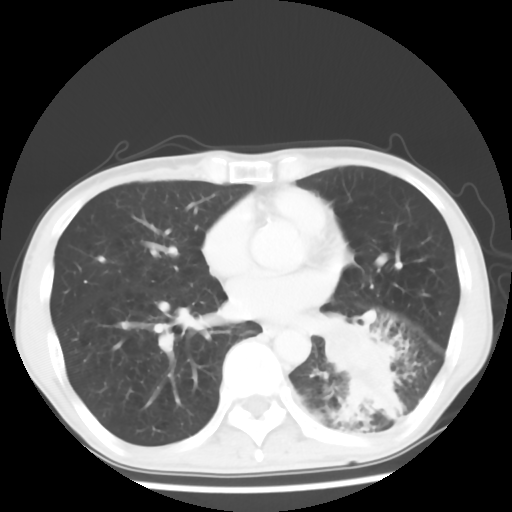
Chest CT, one axial slice. Position 27 of 64 along the scan axis. Reconstruction kernel STANDARD. Lung window (W 1500 / L -600 HU). 5 mm slice thickness. 512 × 512 image matrix, field of view 313 × 313 mm. Patient: male, 68 years. From the clinical record (not read from this slice): clinical TNM (as recorded): T4 N0 M0.
Structures marked on this image (rectangle marked by the reading radiologist):
- lung tumour (recorded histology: squamous cell carcinoma): bounding box (x1, y1, x2, y2) in pixels: (312, 300, 411, 419)